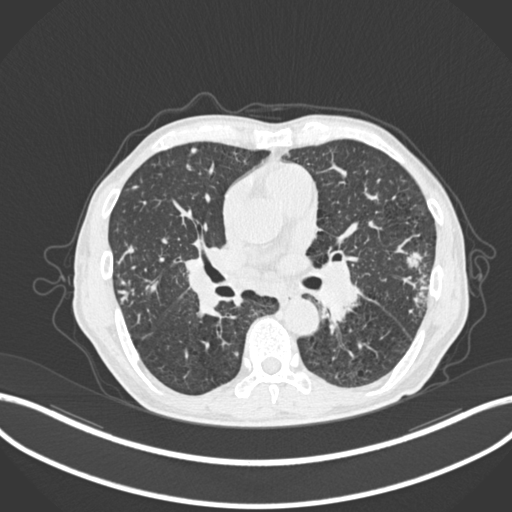
Chest CT, one axial slice. Slice 120 of 287 in the series (ordered by position). Lung window (W 1500 / L -600 HU). 1 mm slice thickness. 512 × 512 image matrix, field of view 400 × 400 mm. Patient: male, 74 years. Case-level facts recorded for this patient, not image findings: clinical TNM (as recorded): T2a N1 M0.
Structures marked on this image (rectangle marked by the reading radiologist):
- lung tumour (recorded histology: adenocarcinoma): bounding box [x1, y1, x2, y2] px = [401, 248, 424, 271]